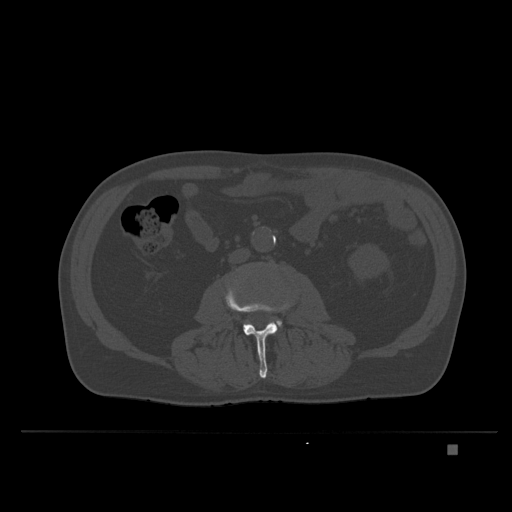
CT including the spine, one axial slice; bone window (W 1800 / L 400 HU); 1.5 mm slice thickness; 512 × 512 image matrix, field of view 434 × 434 mm. Male patient, age 73 years. Case-level facts recorded for this patient, not image findings: primary cancer: skin.
Annotated regions visible in this slice (semi-automatic segmentation, software-assisted and operator-edited):
- L3 vertebra: bounding box [x1, y1, x2, y2] px = [225, 276, 291, 378]
- L4 vertebra: [269, 319, 281, 324]